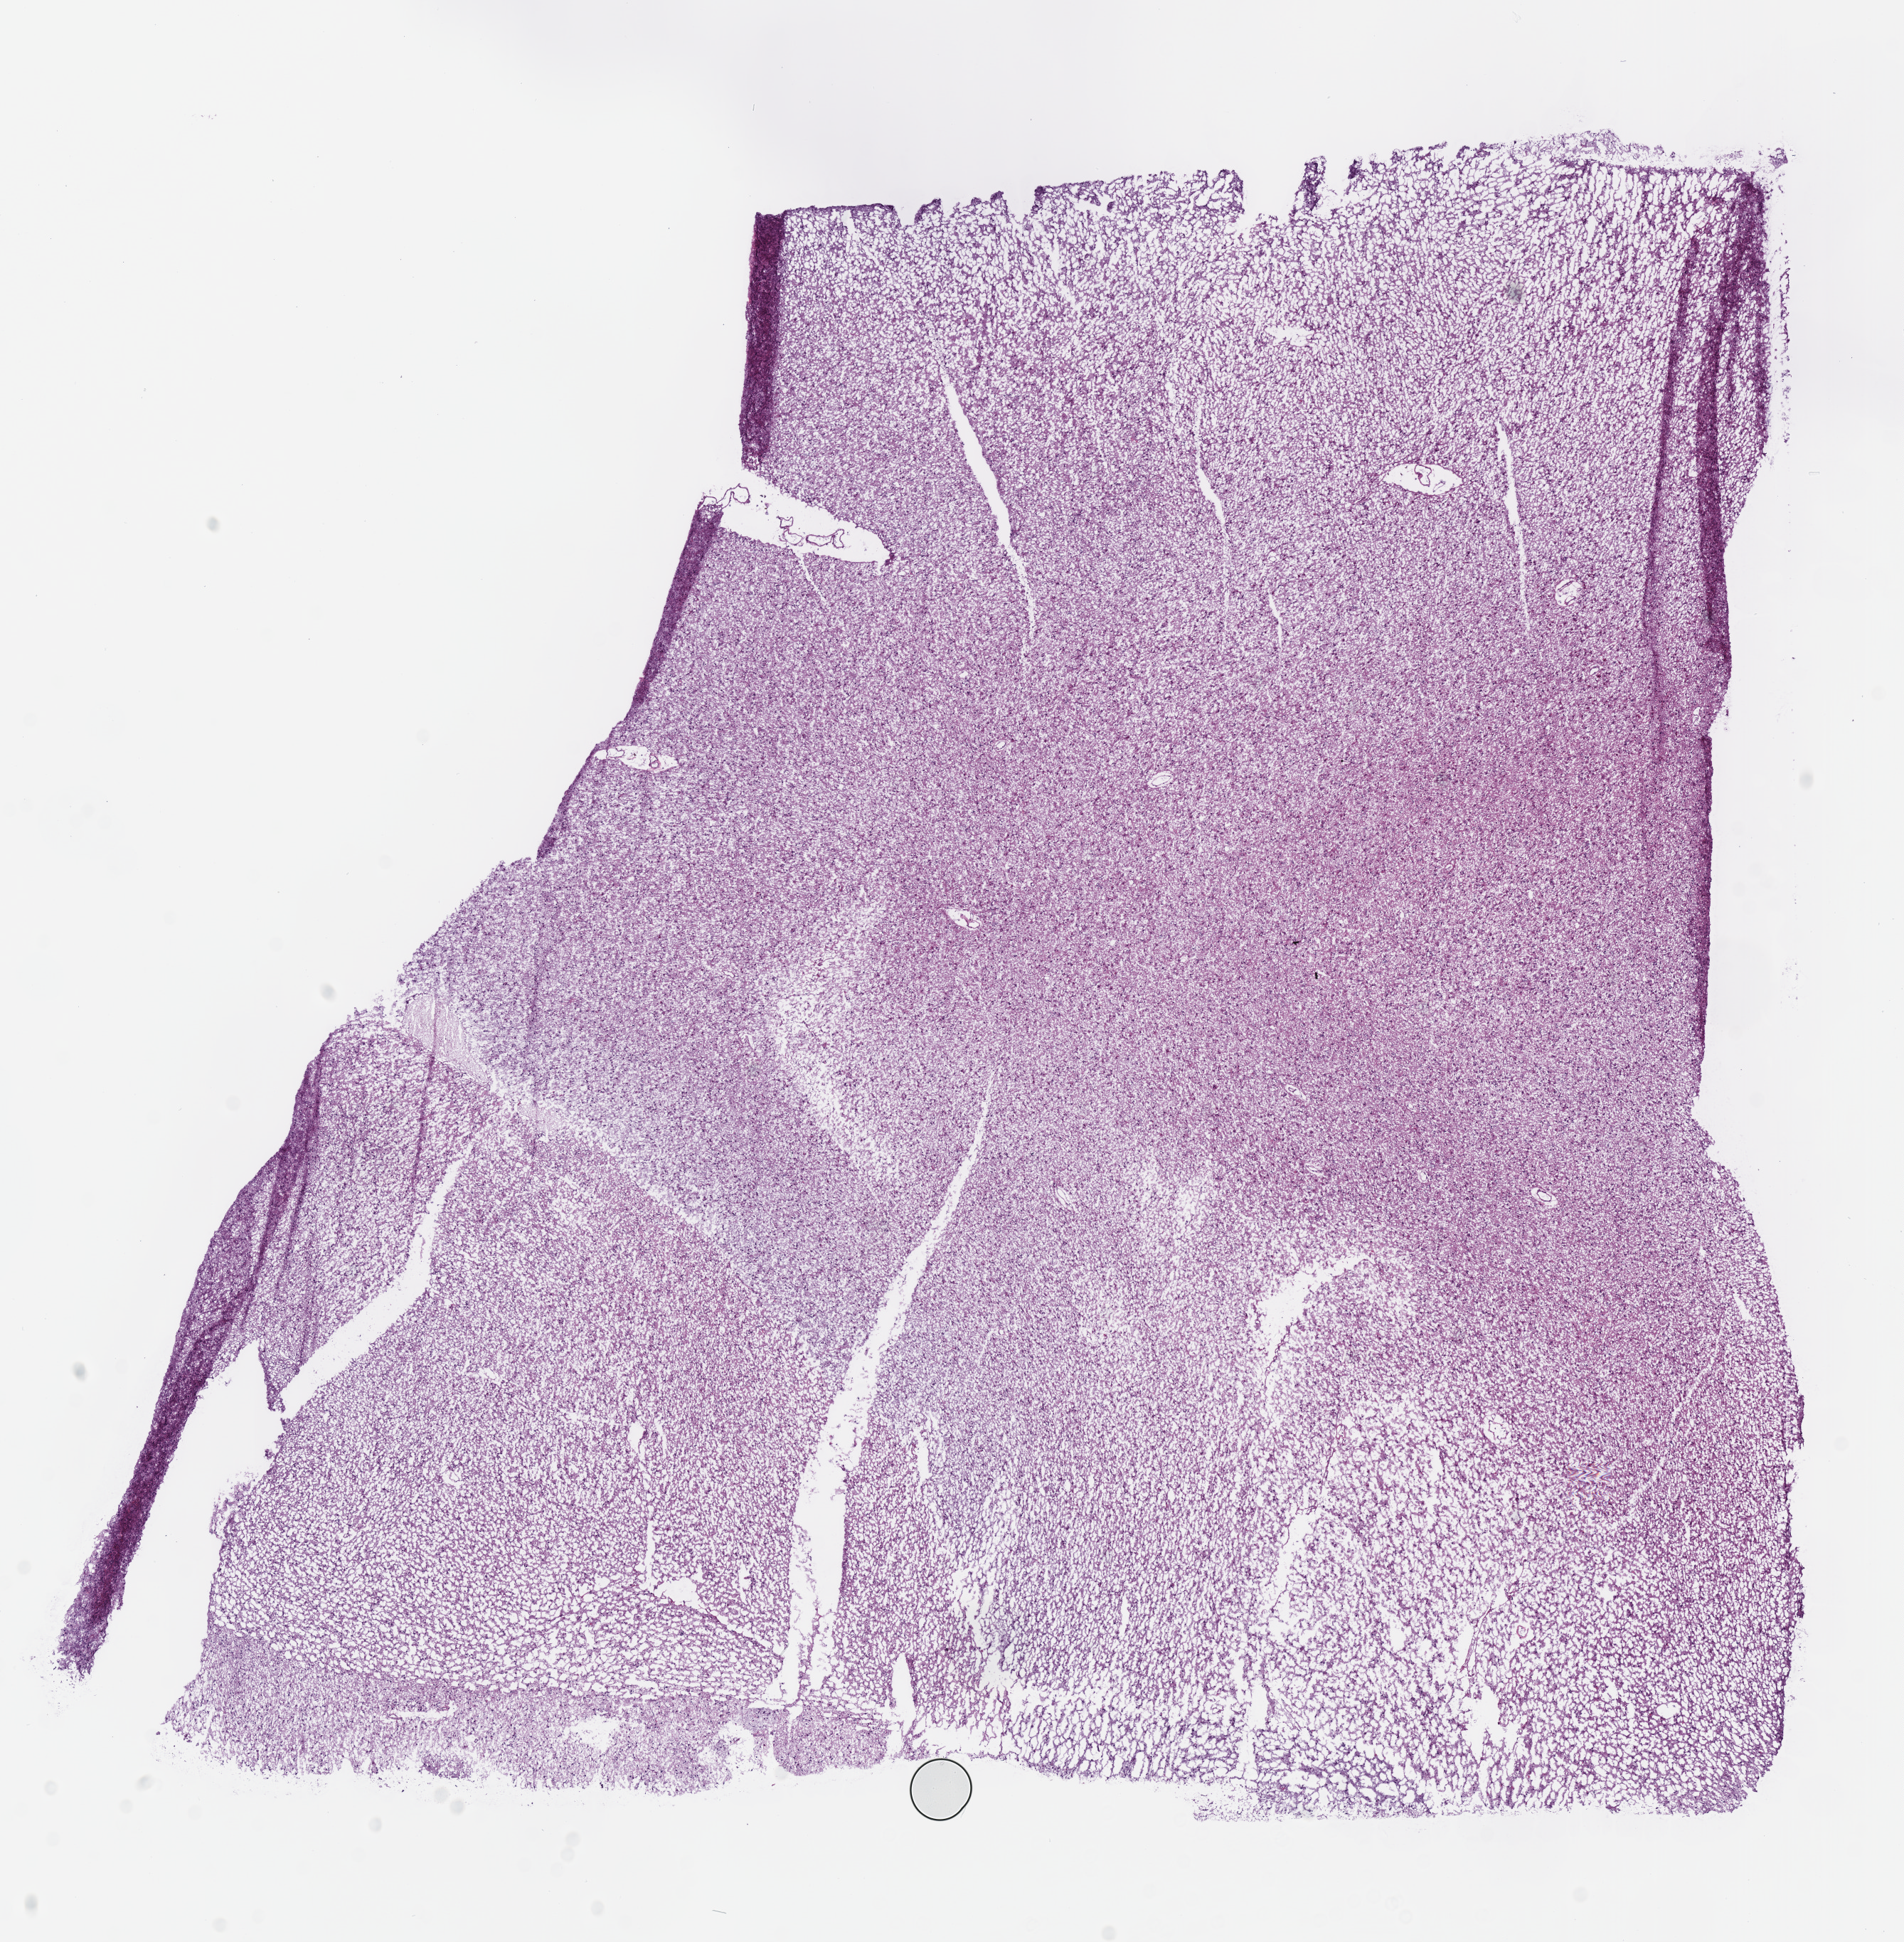
Digitized H&E tissue section (whole slide) — whole scanned area (about 10.5 x 10.8 mm, from a 40x scan) shown as a low-resolution overview, frozen section from the bottom of the tissue portion, primary tumour sample from the brain. Female patient; age at initial diagnosis 58 years. Histologic grade: G2 (moderately differentiated). Composition of this section per pathologist review: tumour cells 100%, tumour nuclei 70%, normal cells 0%, stromal cells 0%, necrosis 0%.
Pathologic diagnosis: Oligodendroglioma, NOS (cerebrum).